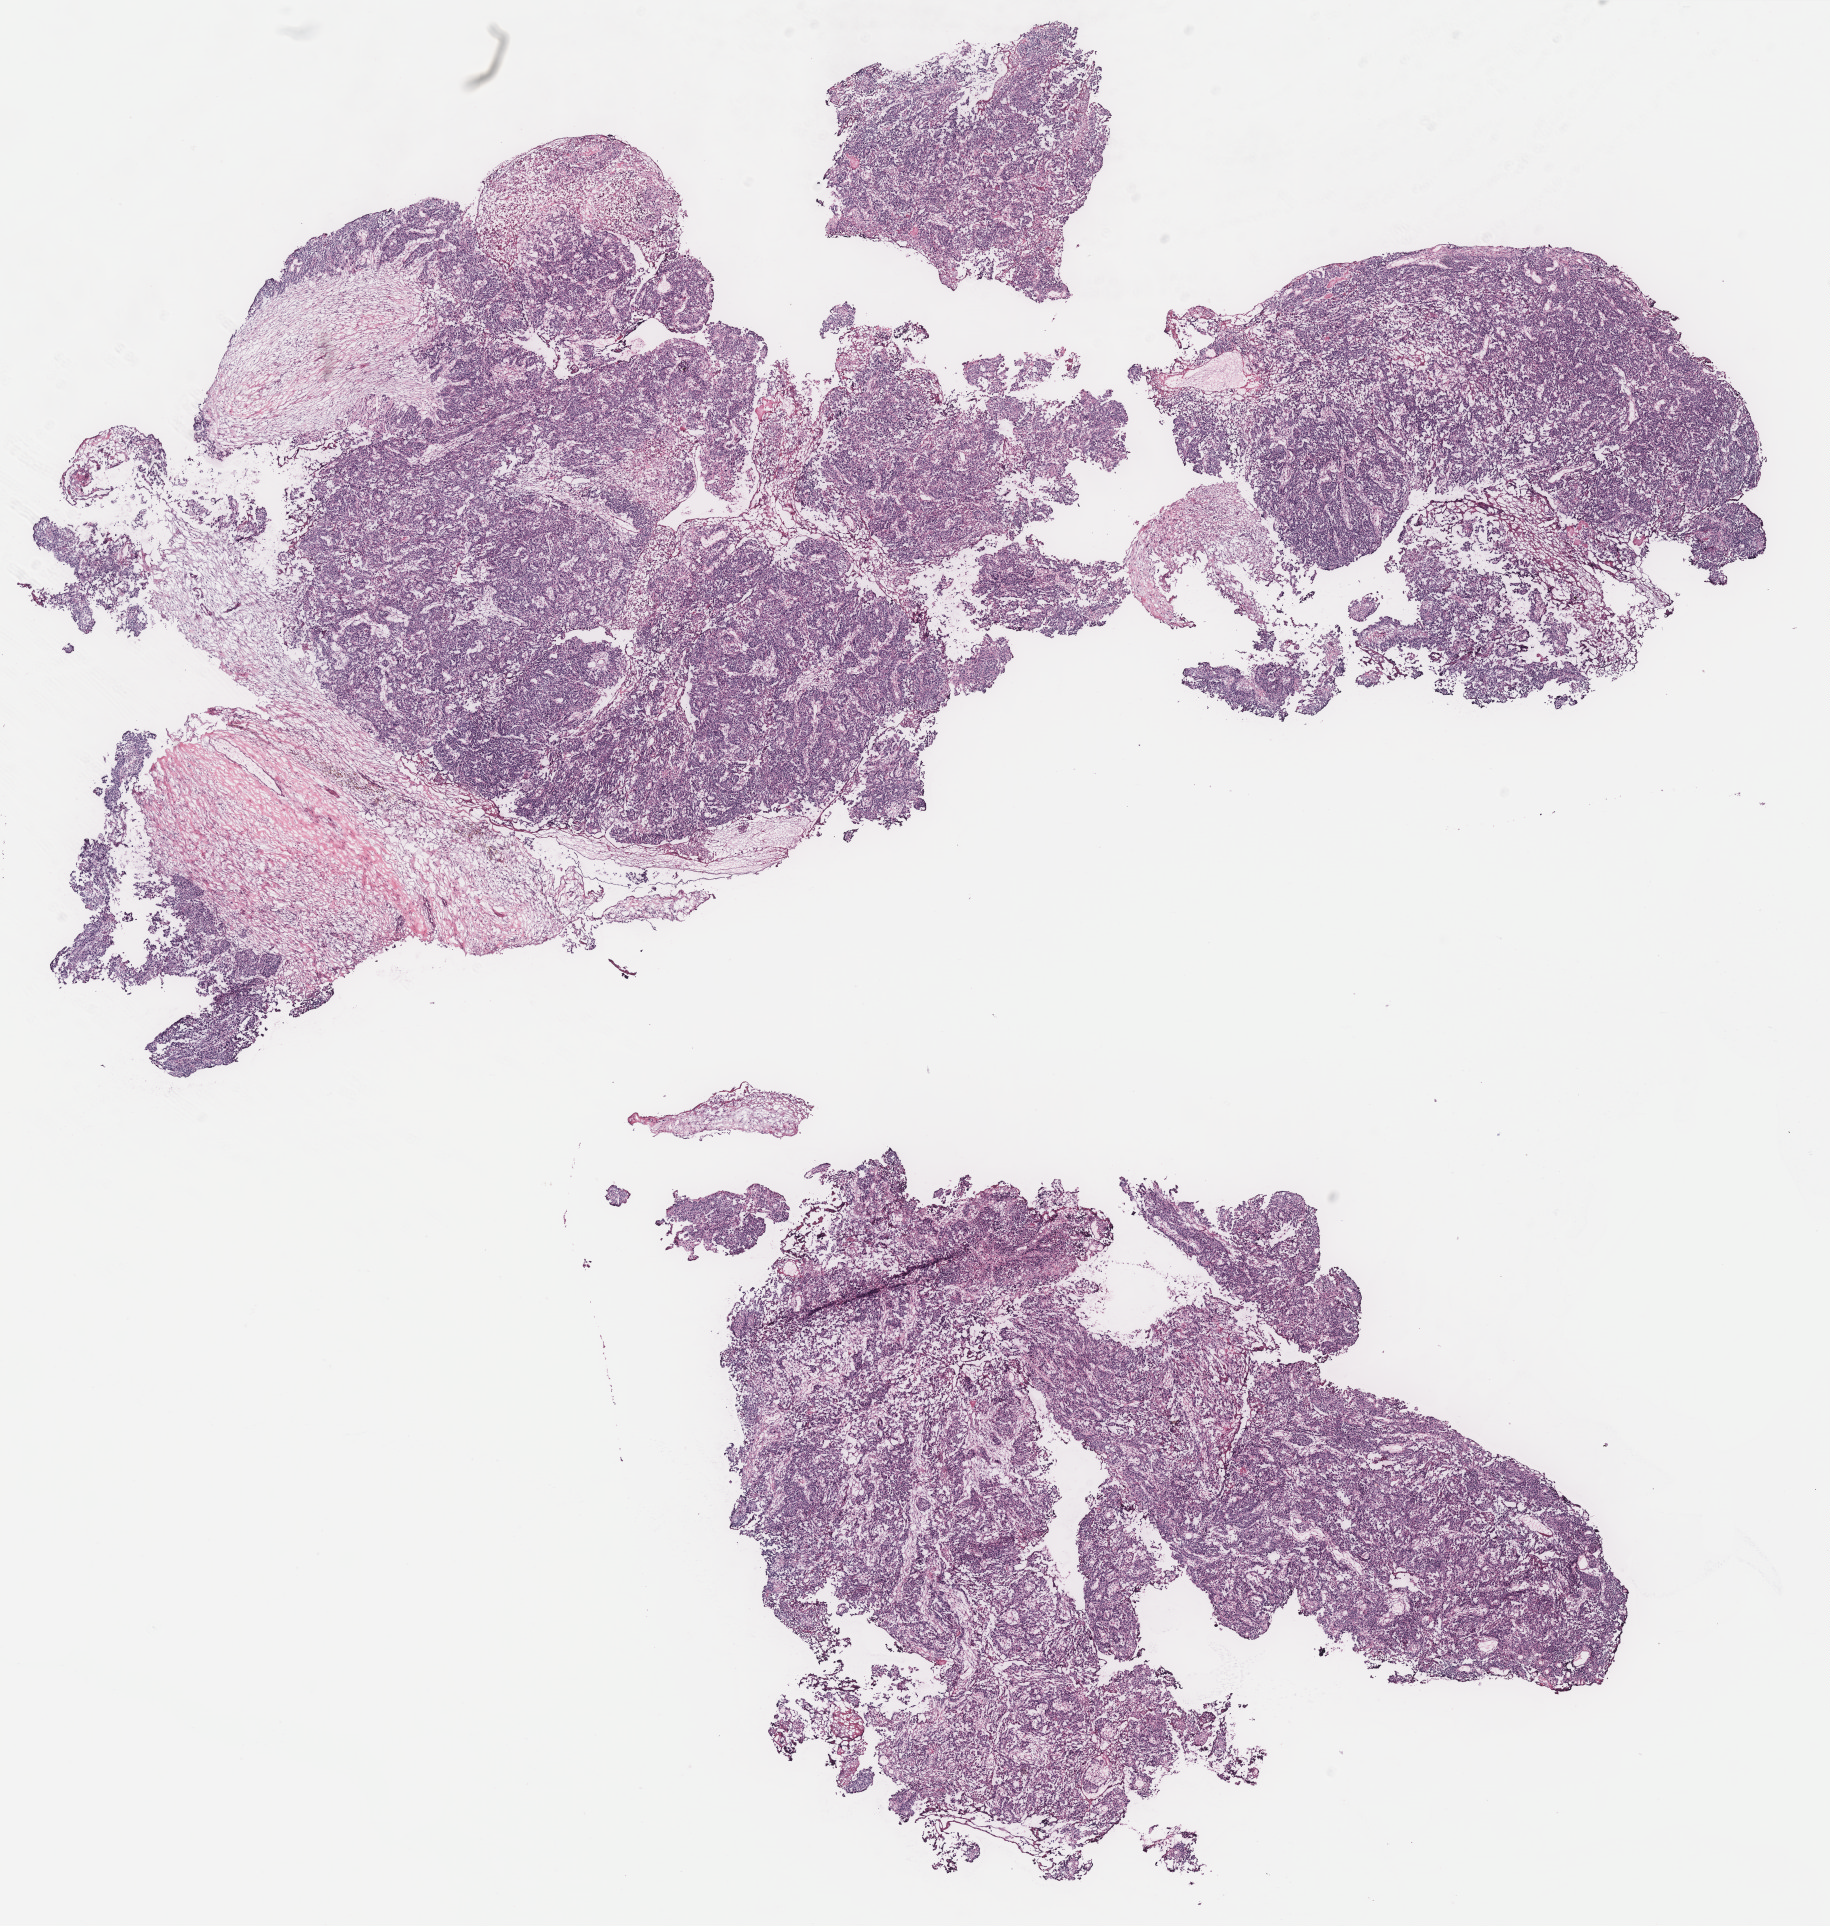
Digitized H&E-stained tissue section (whole slide) — a low-resolution overview of the entire scanned area, about 14.6 x 15.4 mm. Ovary, tumour tissue. Female, 66 y/o.
Primary tumour site (as recorded): peritoneum. Histologic diagnosis: Serous adenocarcinoma, NOS (peritoneum, NOS).